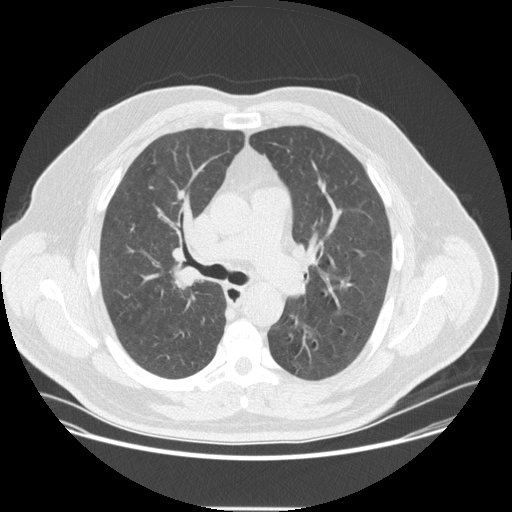
Axial slice from a low-dose chest CT screening exam. Second screening round (one year after baseline). Lung window (W 1500 / L -600 HU). Male participant, aged 57 years at enrolment. Current smoker at enrolment.
Lesion marked by an expert reader, bounding box [x1, y1, x2, y2] px = [156, 255, 211, 304]. Screening reader's record for this exam (one nodule recorded; not confirmed to be the boxed lesion): non-calcified nodule or mass ≥4 mm, right upper lobe, 20 × 16 mm, spiculated (stellate) margins, soft tissue attenuation, pre-existing on the prior screen: no. Official screen result: positive, other.